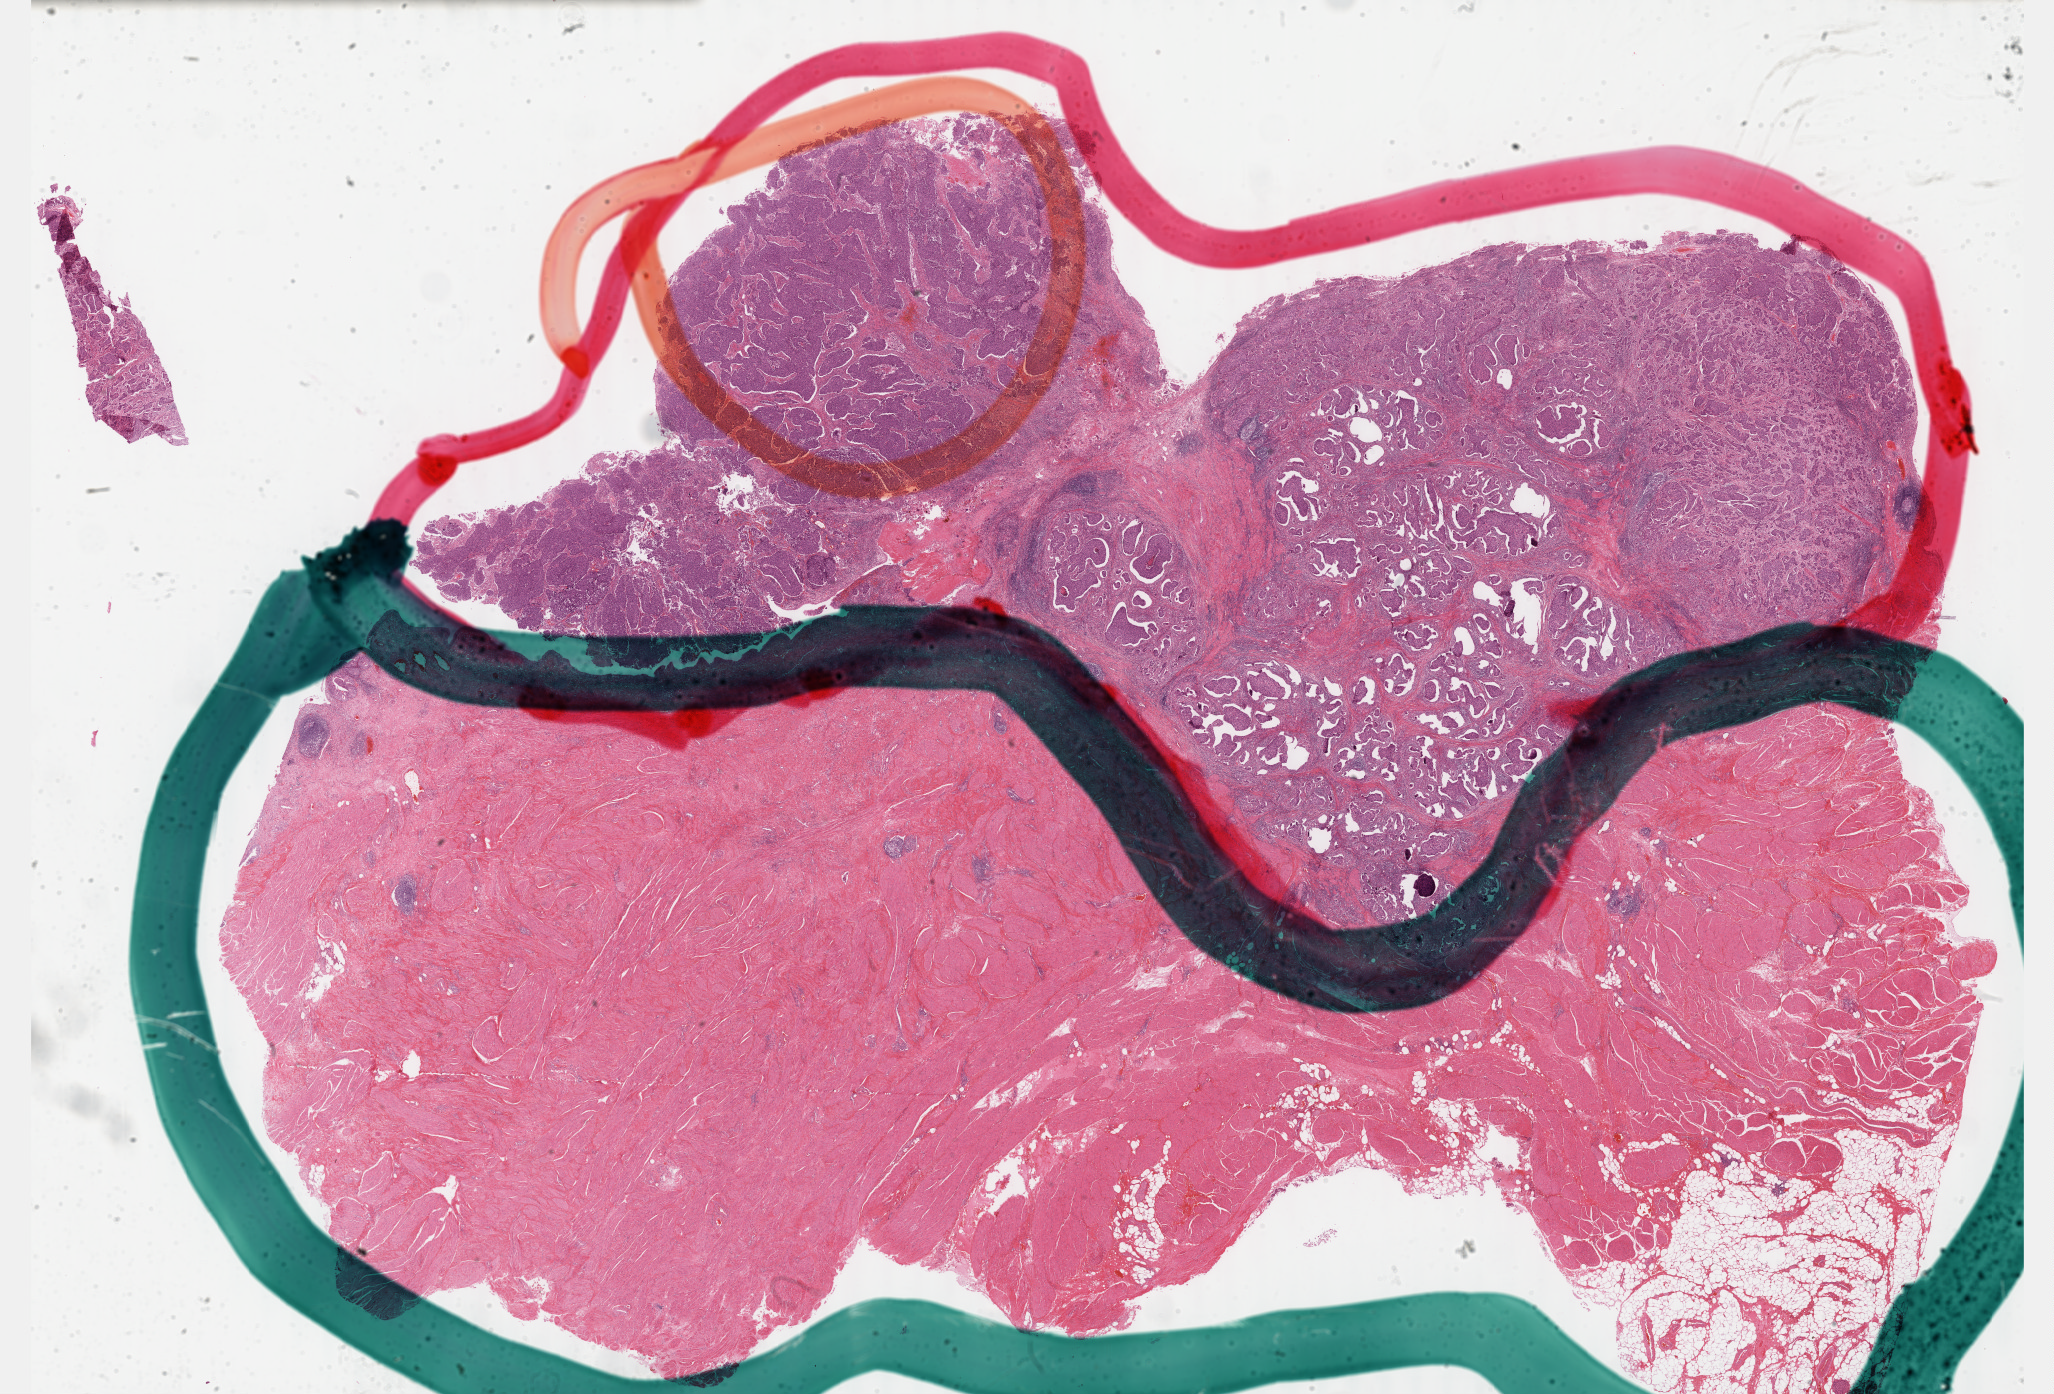
H&E whole-slide image, shown as a low-resolution overview of the whole scanned area (about 33.2 x 22.5 mm, acquisition: 40x scan); FFPE section; sample: primary tumour, bladder. Male, age 64 years at initial diagnosis. Histologic grade: high grade.
TNM: T3 N0 M0. Lymph nodes positive (case pathology): 0 of 2 examined. AJCC pathologic stage: III (7th edition). Pathologic diagnosis: Transitional cell carcinoma.